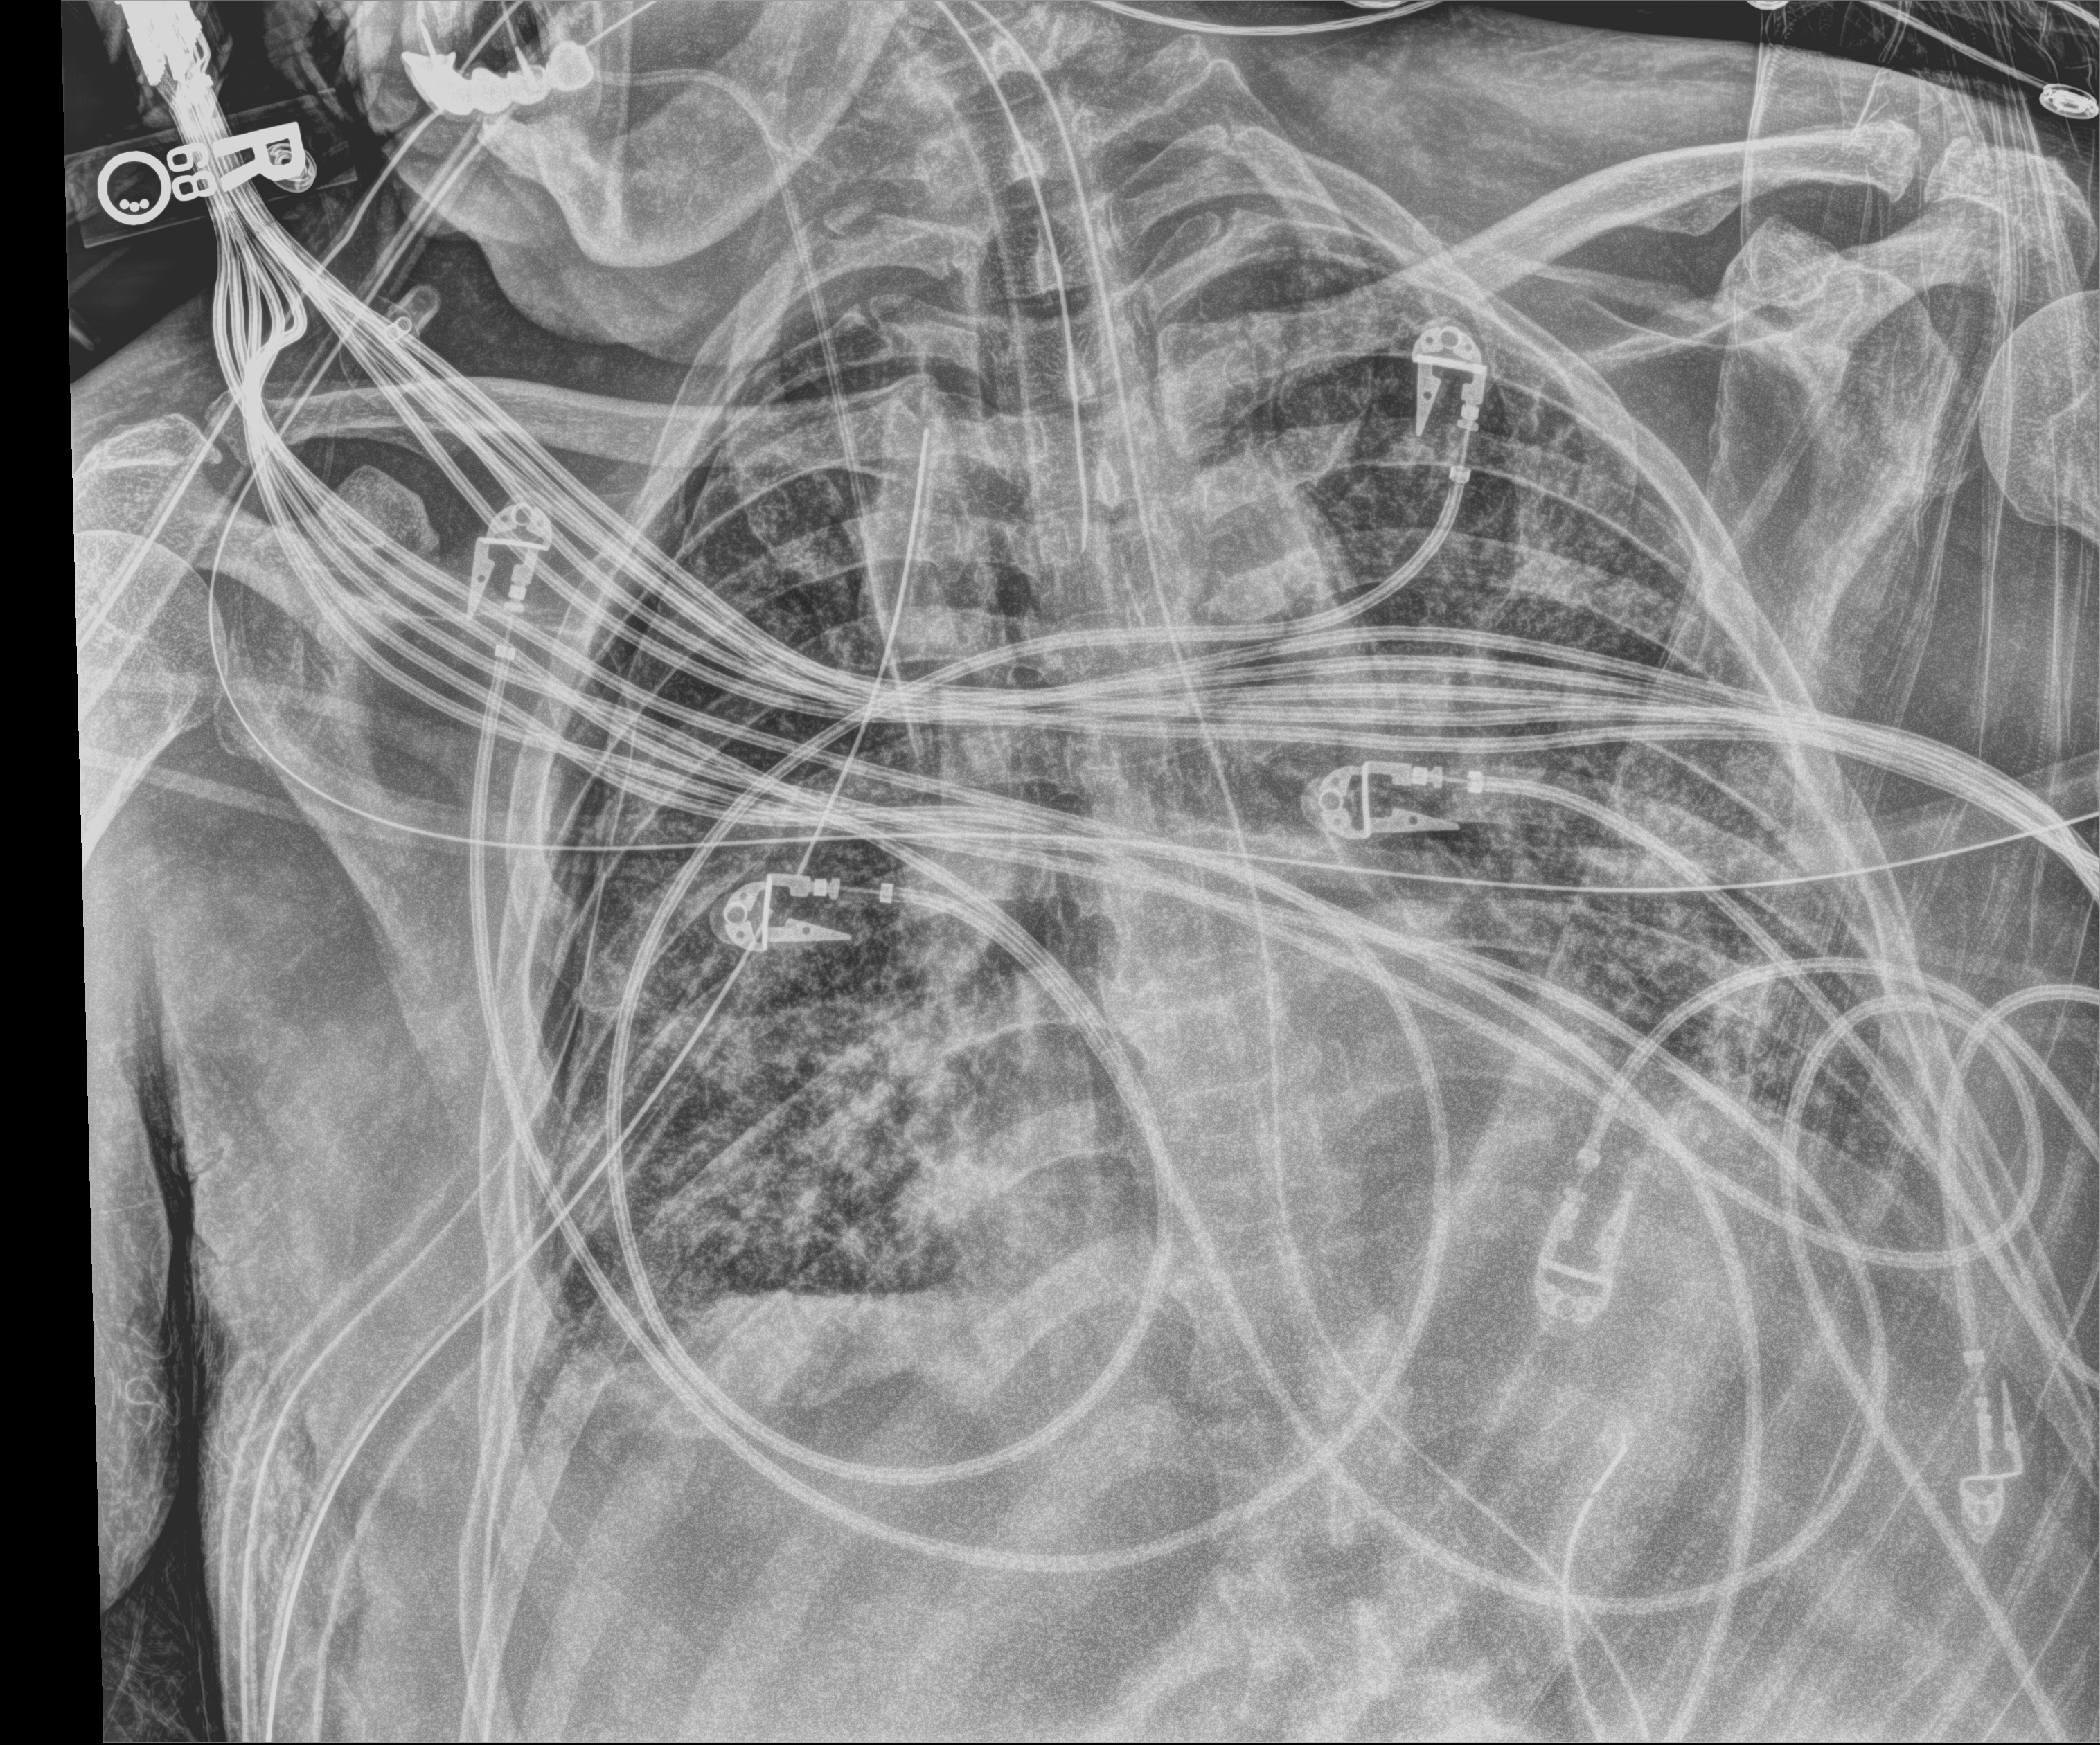
Portable chest radiograph, anteroposterior (AP) projection. Male patient hospitalised with COVID-19, age 60–74 years.
Hospital-stay facts (about this admission, not read from this image; timing relative to this image not recorded):
- hypertension (admission record): yes
- admitted to intensive care during this hospital stay: yes
- mechanically ventilated during this hospital stay: yes